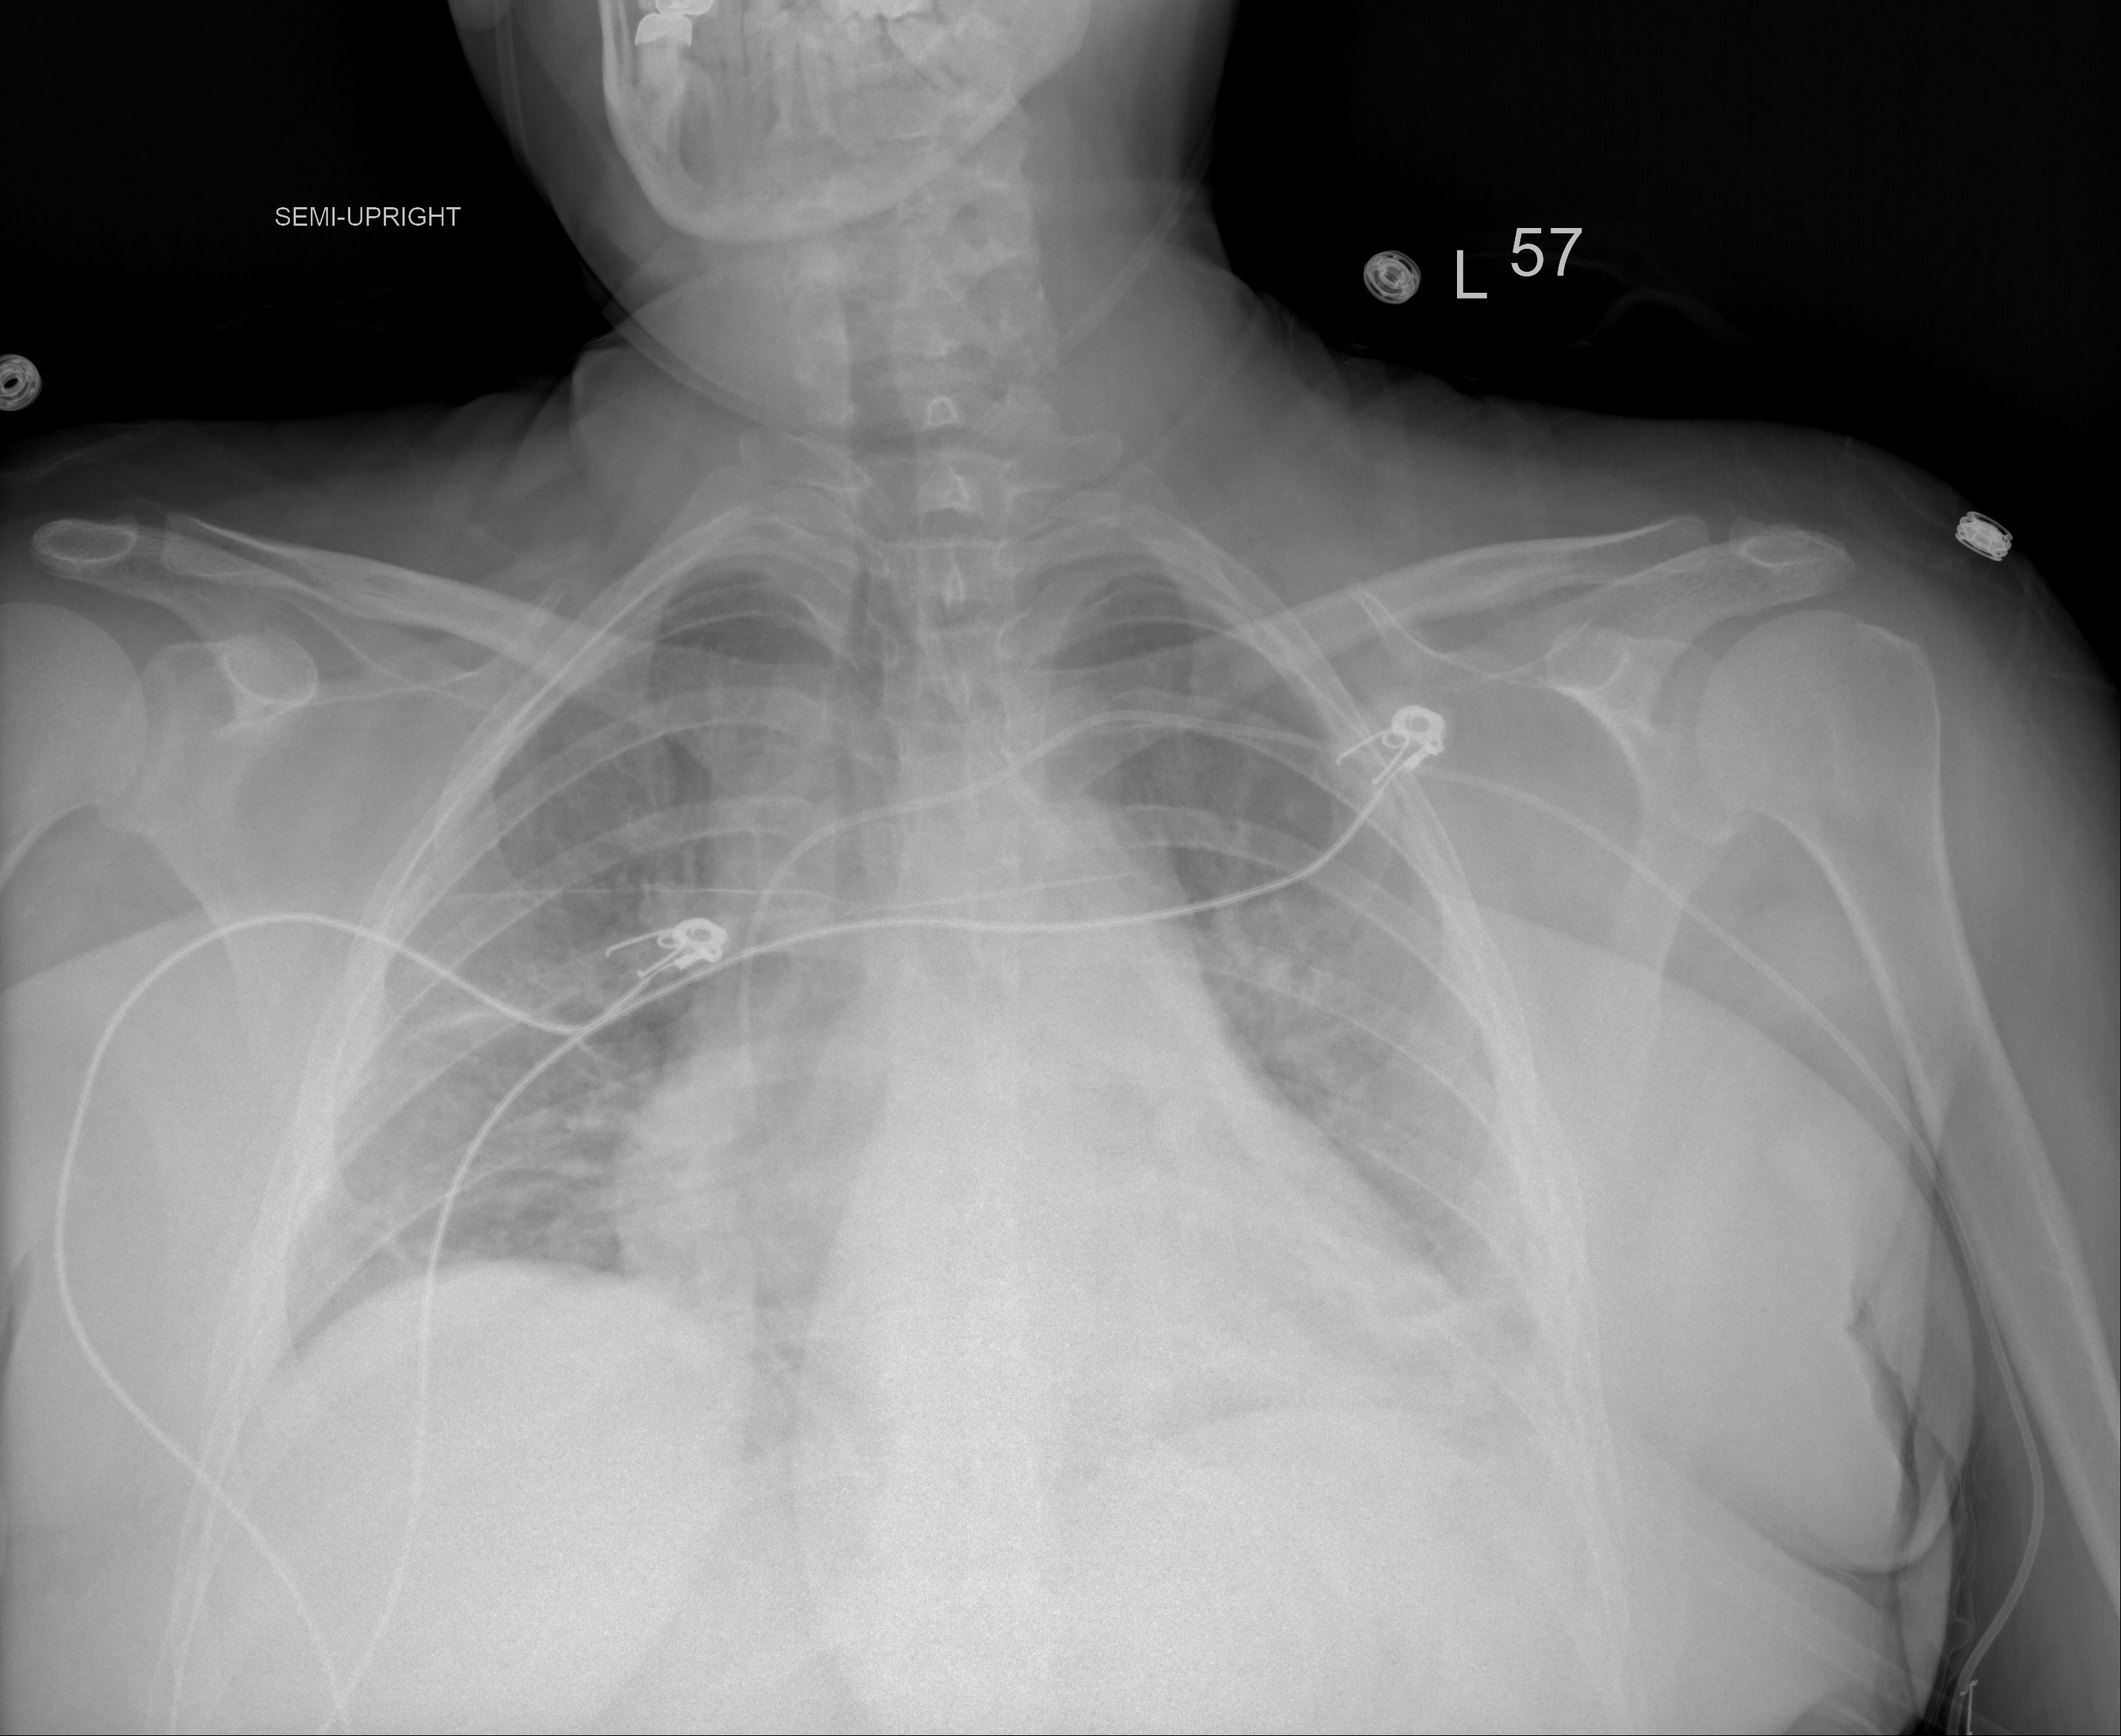
Chest X-ray (portable), AP projection. Female patient, age 29 years; COVID-19 (test-positive).
Key findings recorded by the radiologist: Mild bibasilar airspace disease, slightly improved on the right.